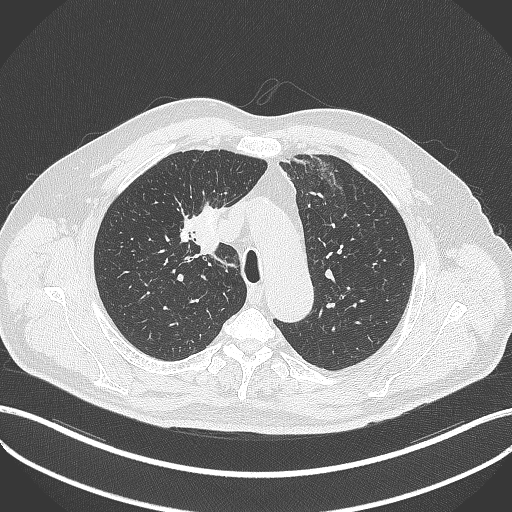
Chest CT, one axial slice. Position 289 of 411 along the scan axis. Lung window (W 1500 / L -600 HU). 1 mm slice thickness. 512 × 512 image matrix, field of view 400 × 400 mm. Patient: male, 60 years. Case-level facts recorded for this patient, not image findings: clinical TNM (as recorded): T1b N1 M0.
Outlined on this slice (rectangle marked by the reading radiologist):
- lung tumour (recorded histology: squamous cell carcinoma): bounding box (x1, y1, x2, y2) in pixels: (188, 196, 224, 259)